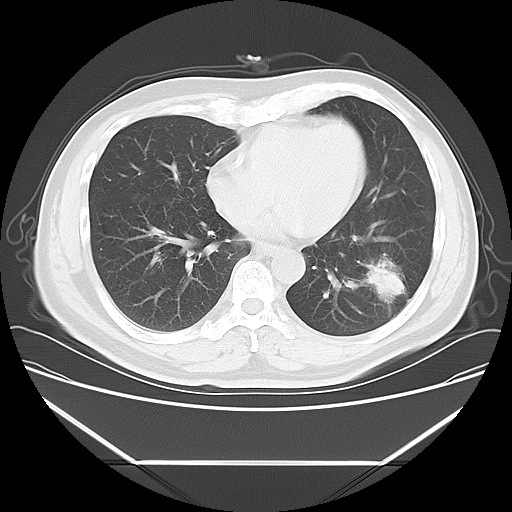
Chest CT, one axial slice; position 23 of 57 along the scan axis; 120 kVp; lung window (W 1500 / L -600 HU); 5 mm slice thickness; 512 × 512 image matrix, field of view 384 × 384 mm. Male patient, age 53 years. Case-level facts recorded for this patient, not image findings: clinical TNM (as recorded): T1c N0 M0; histopathological grade: G2-3.
Annotated regions visible in this slice (rectangle marked by the reading radiologist):
- lung tumour (recorded histology: adenocarcinoma): bounding box (x1, y1, x2, y2) in pixels: (357, 259, 407, 308)